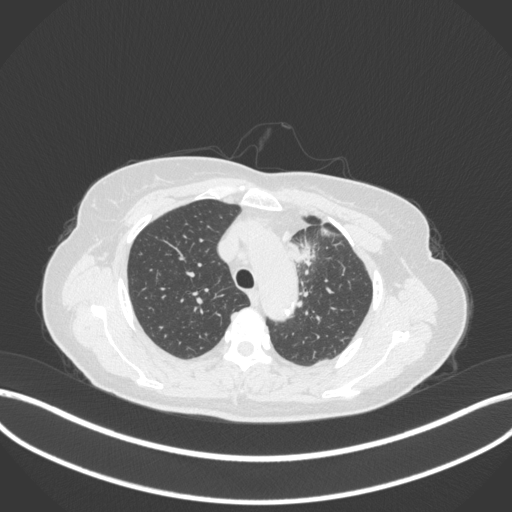
Chest CT, one axial slice; position 255 of 368 along the scan axis; 120 kVp; lung window (W 1500 / L -600 HU); 1 mm slice thickness; 512 × 512 image matrix. Female patient, age 65 years. From the clinical record (not read from this slice): clinical TNM (as recorded): T2a N0 M0; histopathological grade: G2-3.
Annotated regions visible in this slice (rectangle marked by the reading radiologist):
- lung tumour (recorded histology: adenocarcinoma): bounding box <282,236,318,265> (left, top, right, bottom; pixels)